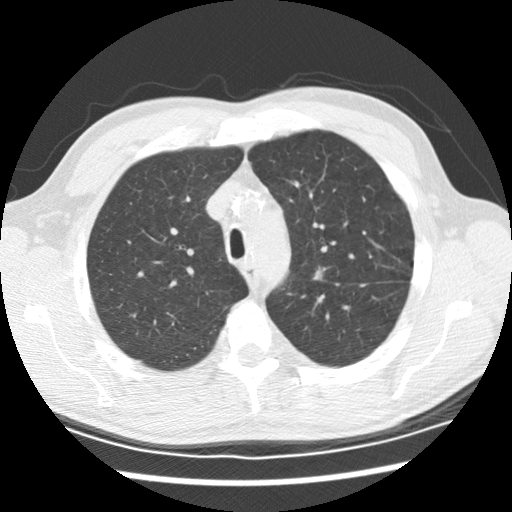
Chest CT (low-dose screening protocol), one axial image; second screening round (one year after baseline); lung window (W 1500 / L -600 HU); 2.5 mm slice thickness; slice 54 of 208 in the series. Male, age 59 years at enrolment. Current smoker at enrolment.
- Expert-annotated lung lesion, bounding box <300,262,336,293> (left, top, right, bottom; pixels).
- Reader record for this screening exam (exam-level; its link to the box is not recorded): non-calcified nodule or mass ≥4 mm, left upper lobe, 8 × 7 mm, spiculated (stellate) margins, soft tissue attenuation, pre-existing on the prior screen: yes; interval growth: yes.
- Participant outcome: lung cancer diagnosed 251 days after this screen — adenocarcinoma, NOS, left upper lobe, left lower lobe, poorly differentiated (G3), stage IV (AJCC 6th edition).